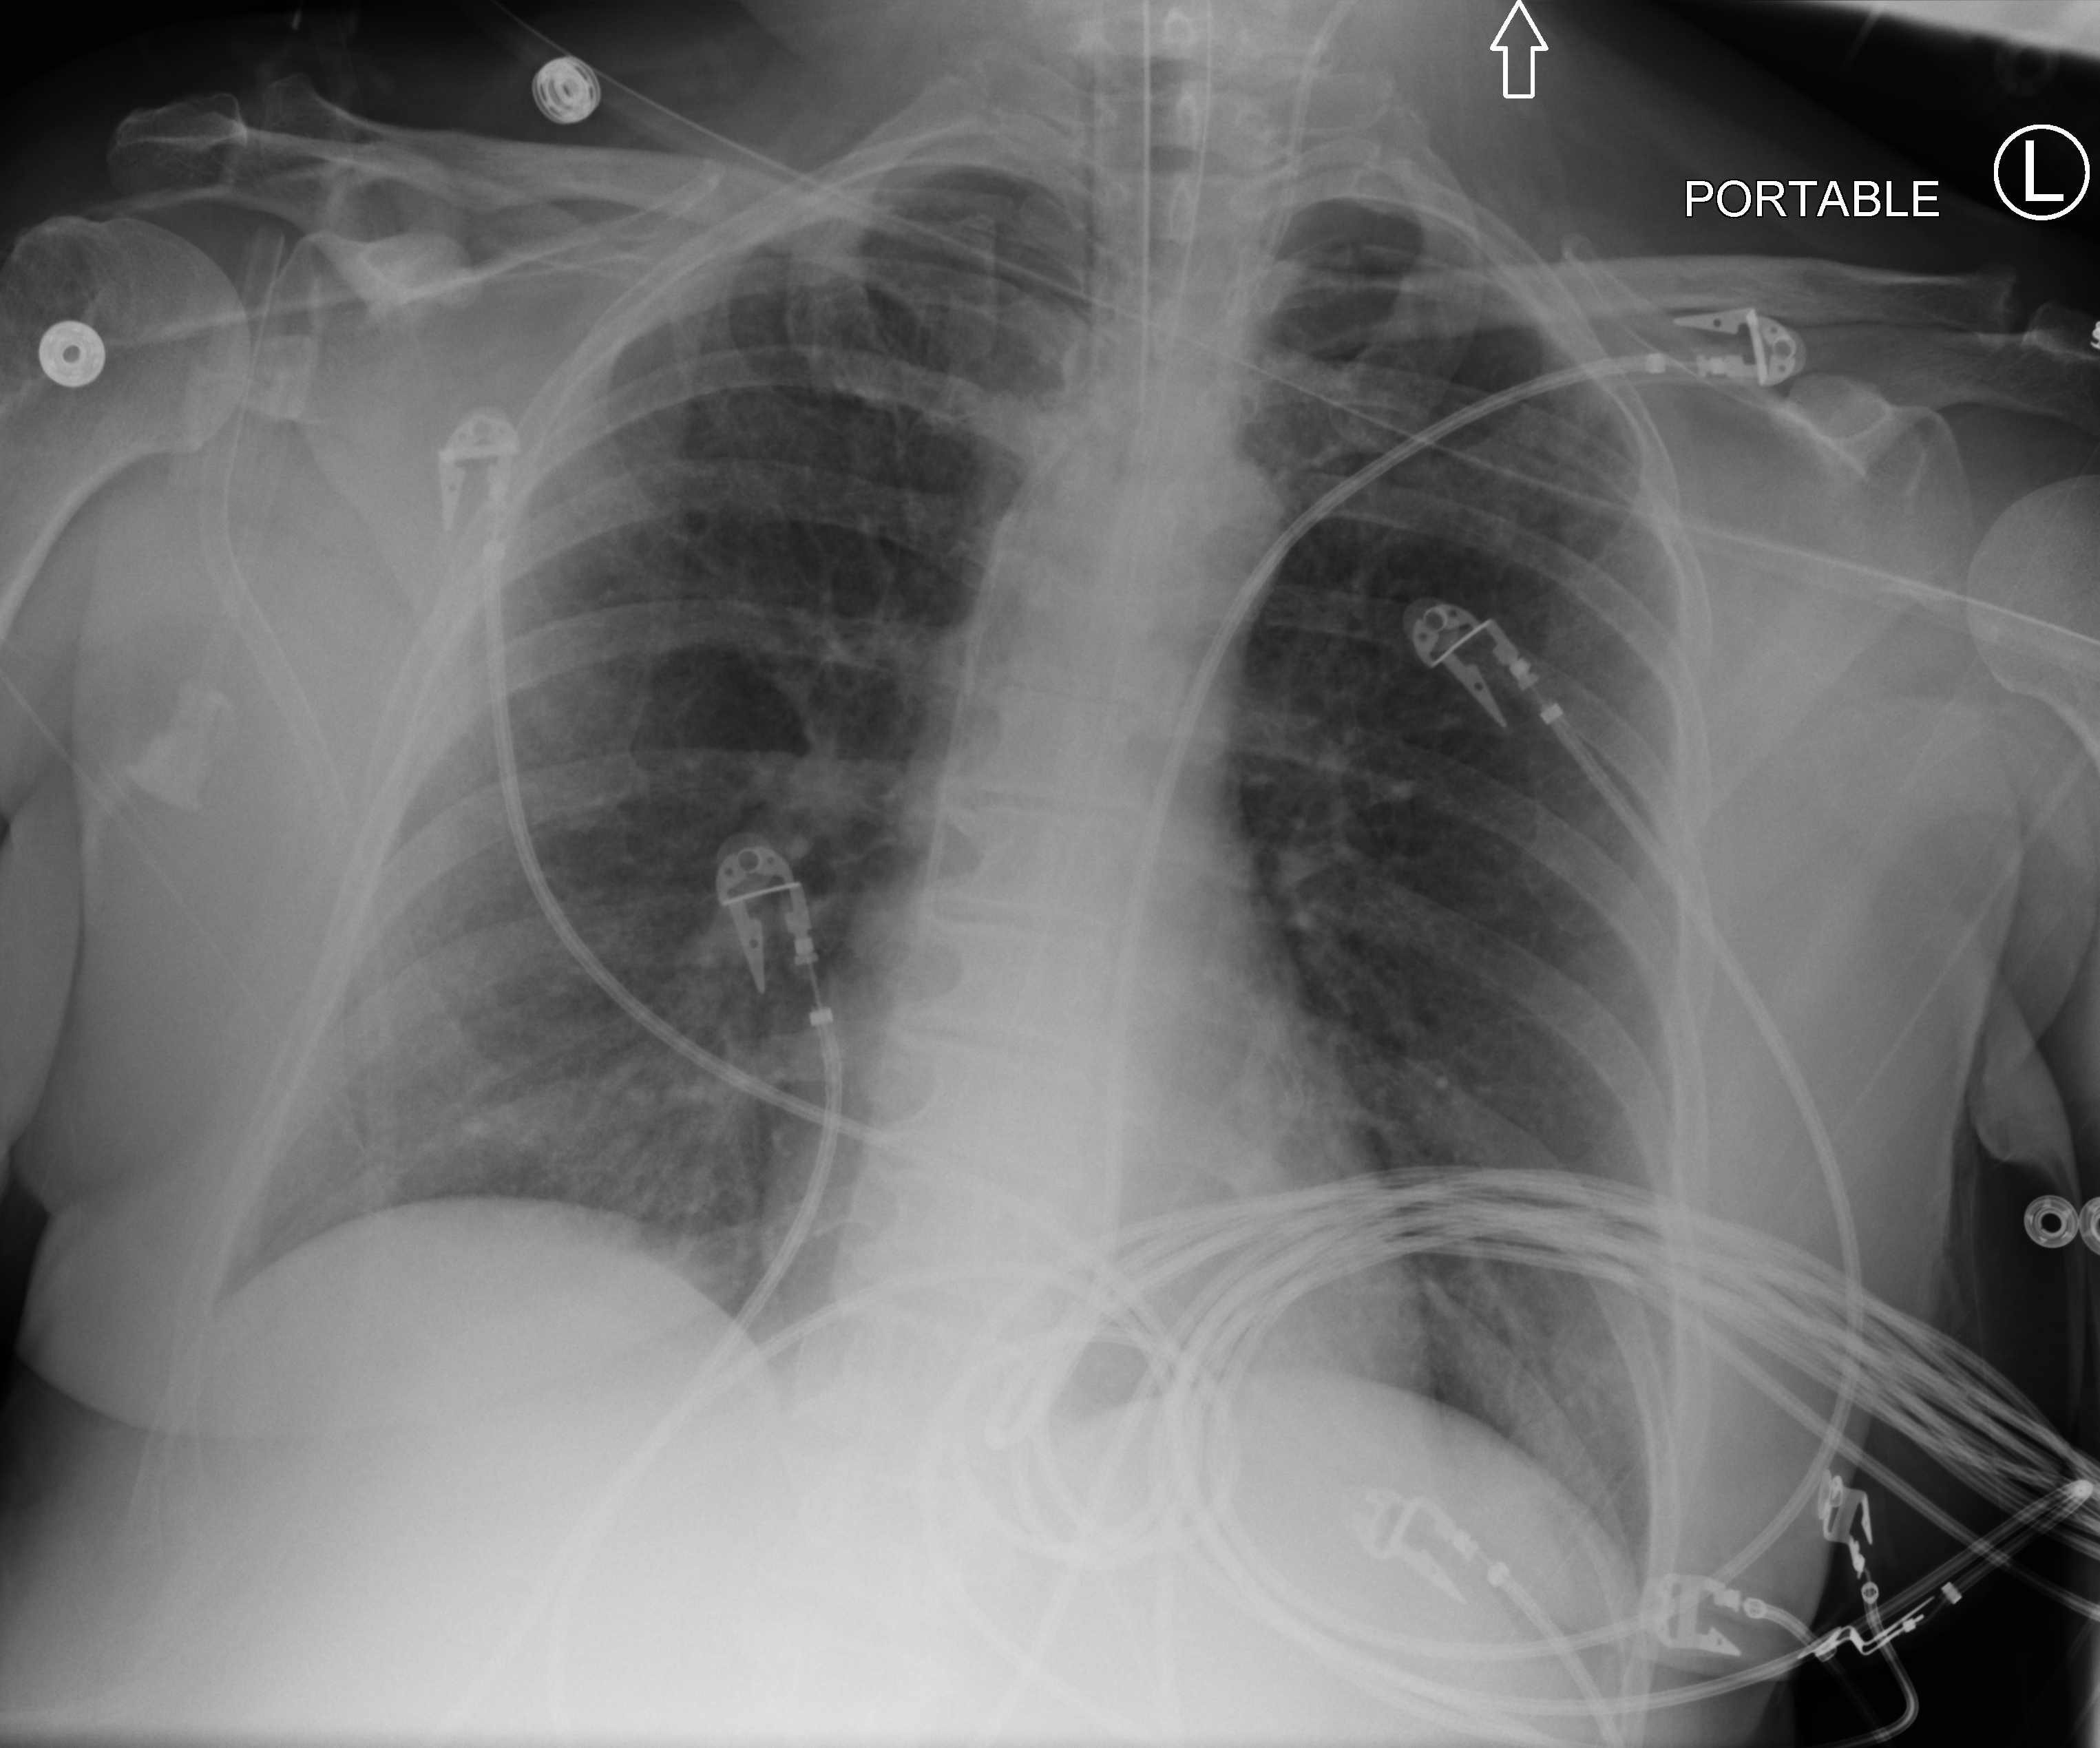
Bedside chest radiograph (computed radiography), anteroposterior (AP) projection. Female patient hospitalised with COVID-19, age 60–74 years.
Admission-level facts for this patient (not findings on this image; timing relative to this image not recorded): mechanically ventilated during this hospital stay: yes.